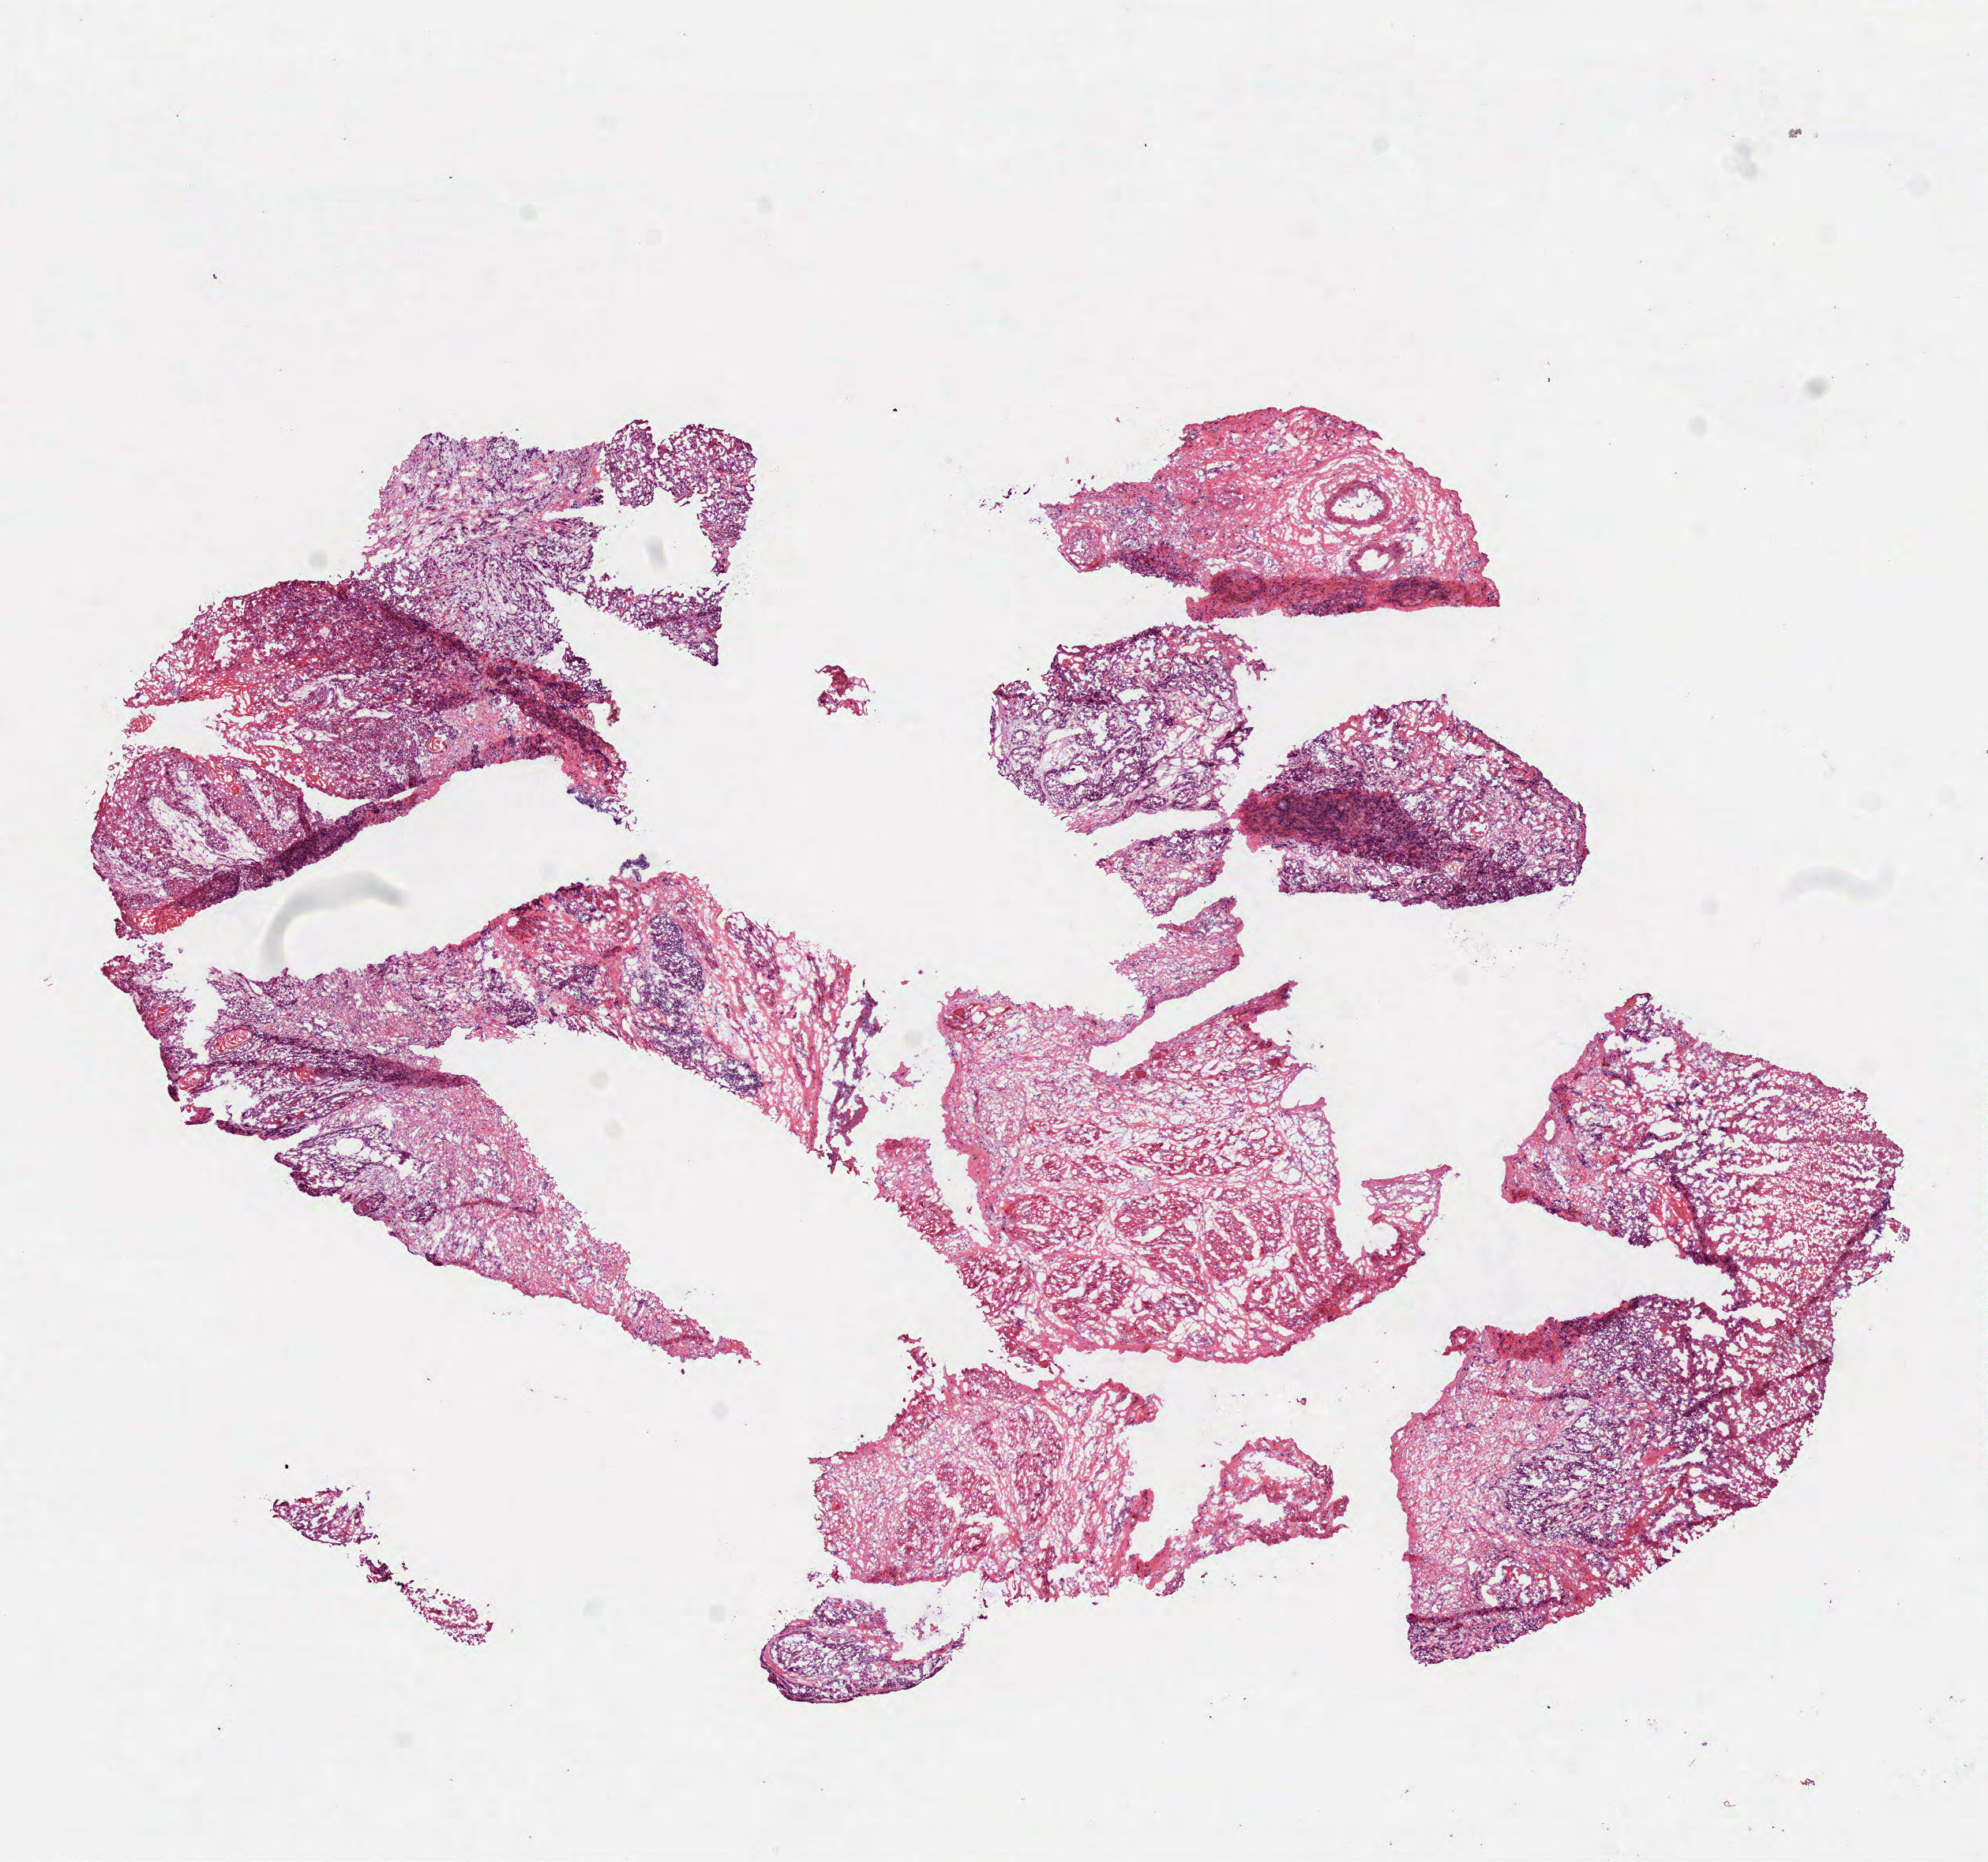
Digitized H&E-stained tissue section (whole slide) — shown as a low-resolution overview of the whole scanned area (about 10.2 x 9.5 mm), frozen section from the bottom of the tissue portion, head and neck, primary tumour sample. Male patient; age at initial diagnosis 55 years. Histologic grade: G2 (moderately differentiated). Composition of this section per pathologist review: tumour cells 75%, tumour nuclei 75%, normal cells 10%, stromal cells 15%, necrosis 0%.
TNM: T3 N0. Histologic diagnosis: Squamous cell carcinoma, NOS (larynx, NOS). AJCC pathologic stage: III (7th edition).